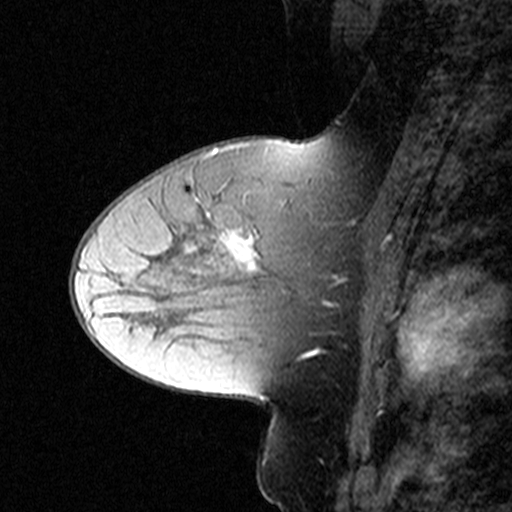
Breast MRI (dynamic contrast-enhanced), one sagittal slice; position 23 of 44 along the scan axis; dynamic contrast-enhanced study with each time point stored as its own series, time point 2 of 3 at this slice position (early post-contrast, ordered by acquisition time); 1.5 T; TE 4.5 ms, TR 11 ms; 3 mm slice thickness; 512 × 512 image matrix, field of view 200 × 200 mm. Patient: female, 50 years. From the clinical record (not read from this slice): setting: breast cancer imaged before/during neoadjuvant chemotherapy; receptor status: HR-positive, HER2-negative.
Structures marked on this image (semi-automatic segmentation, software-assisted and operator-edited):
- analysis volume of interest (the breast-tissue region the enhancement analysis was run in; not a lesion): bounding box (x1, y1, x2, y2) in pixels: (180, 198, 349, 311)
- tumour enhancement mask (voxels above the 90 % enhancement threshold inside the analysis volume of interest): (208, 213, 347, 307)